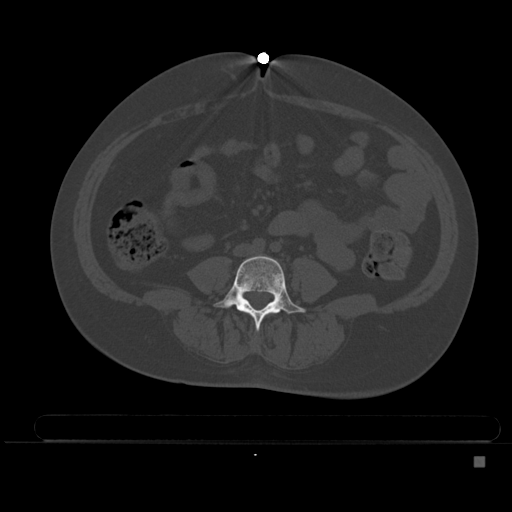
CT including the spine, one axial slice. Position 130 of 495 along the scan axis. Bone window (W 1800 / L 400 HU). 512 × 512 image matrix. Patient: female, 33 years. From the clinical record (not read from this slice): primary cancer: breast; vertebrae with lytic lesions (as recorded): T1.
Outlined on this slice (semi-automatically segmented with operator editing):
- L4 vertebra: bounding box <213,255,306,330> (left, top, right, bottom; pixels)